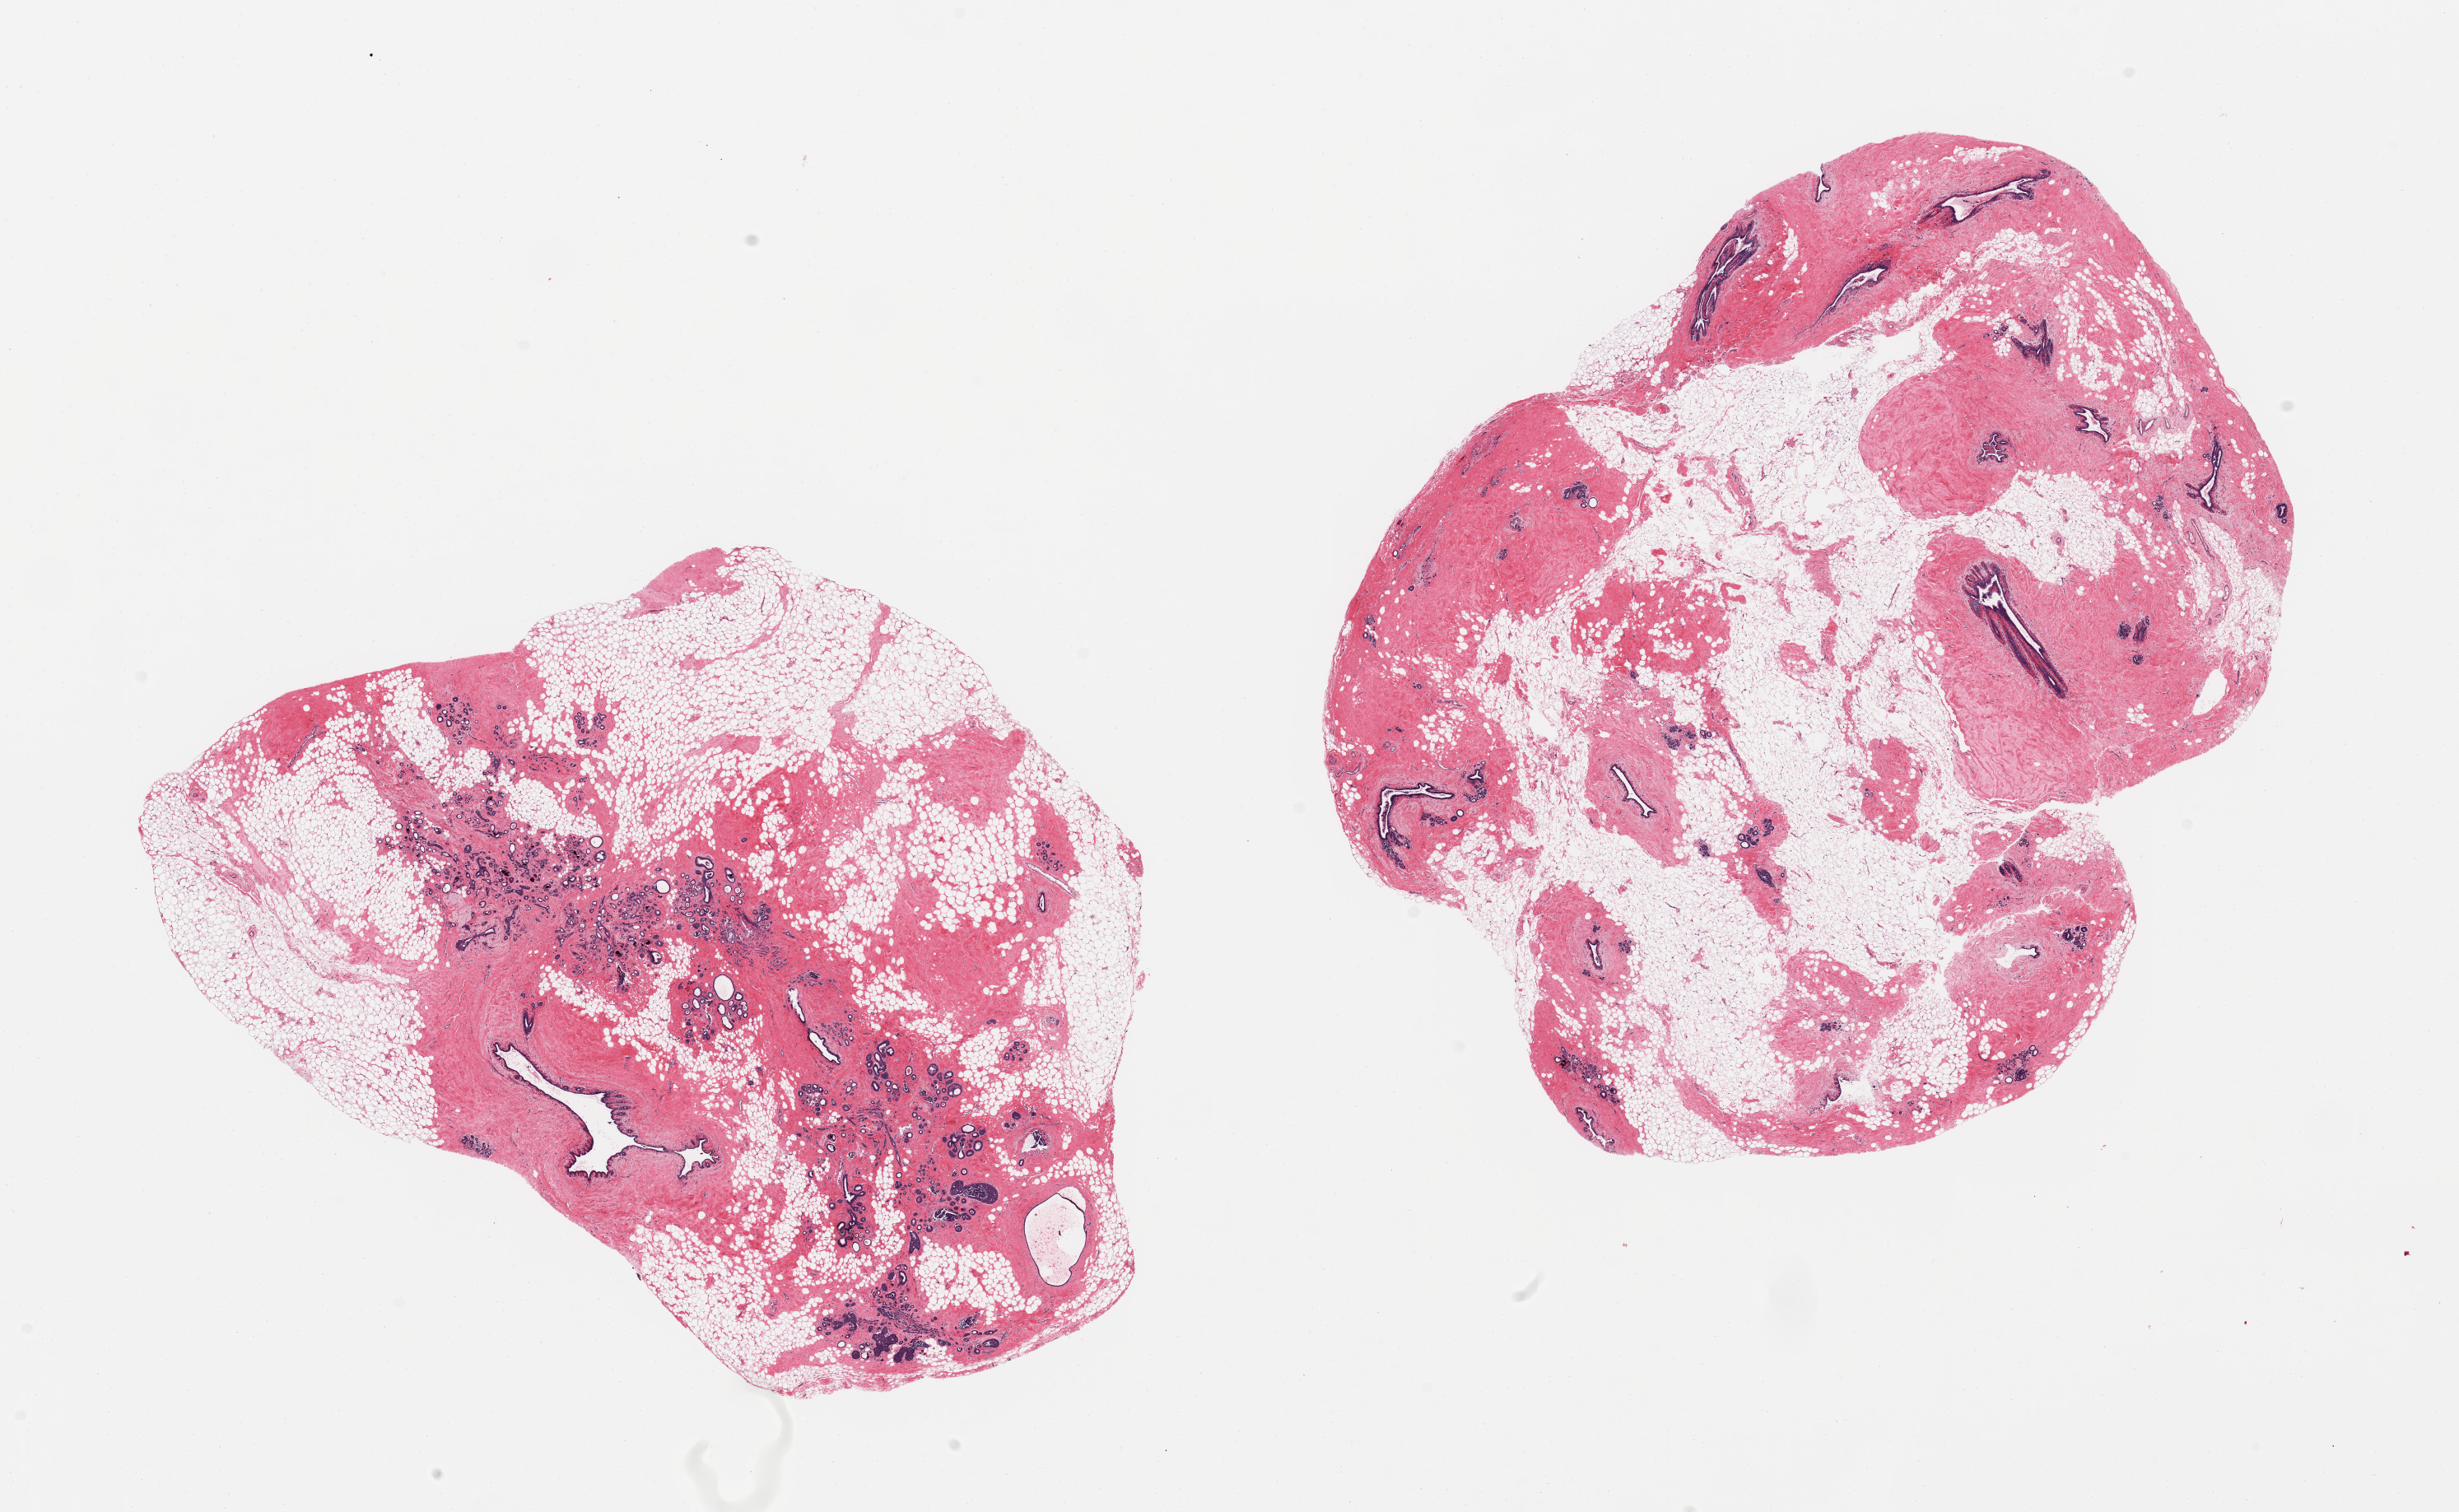
Whole-slide image, haematoxylin and eosin stain — low-resolution overview of the scanned area, about 23.6 x 14.5 mm (acquisition: 20x scan), PAXgene-fixed paraffin-embedded (PFPE) section, section of breast (target tissue), donor tissue sample. Female donor.
Review note (as recorded): 2 pieces, ductal lobular elements well-represented; lobular hyperplasia/atypical hyperplasia noted focally.